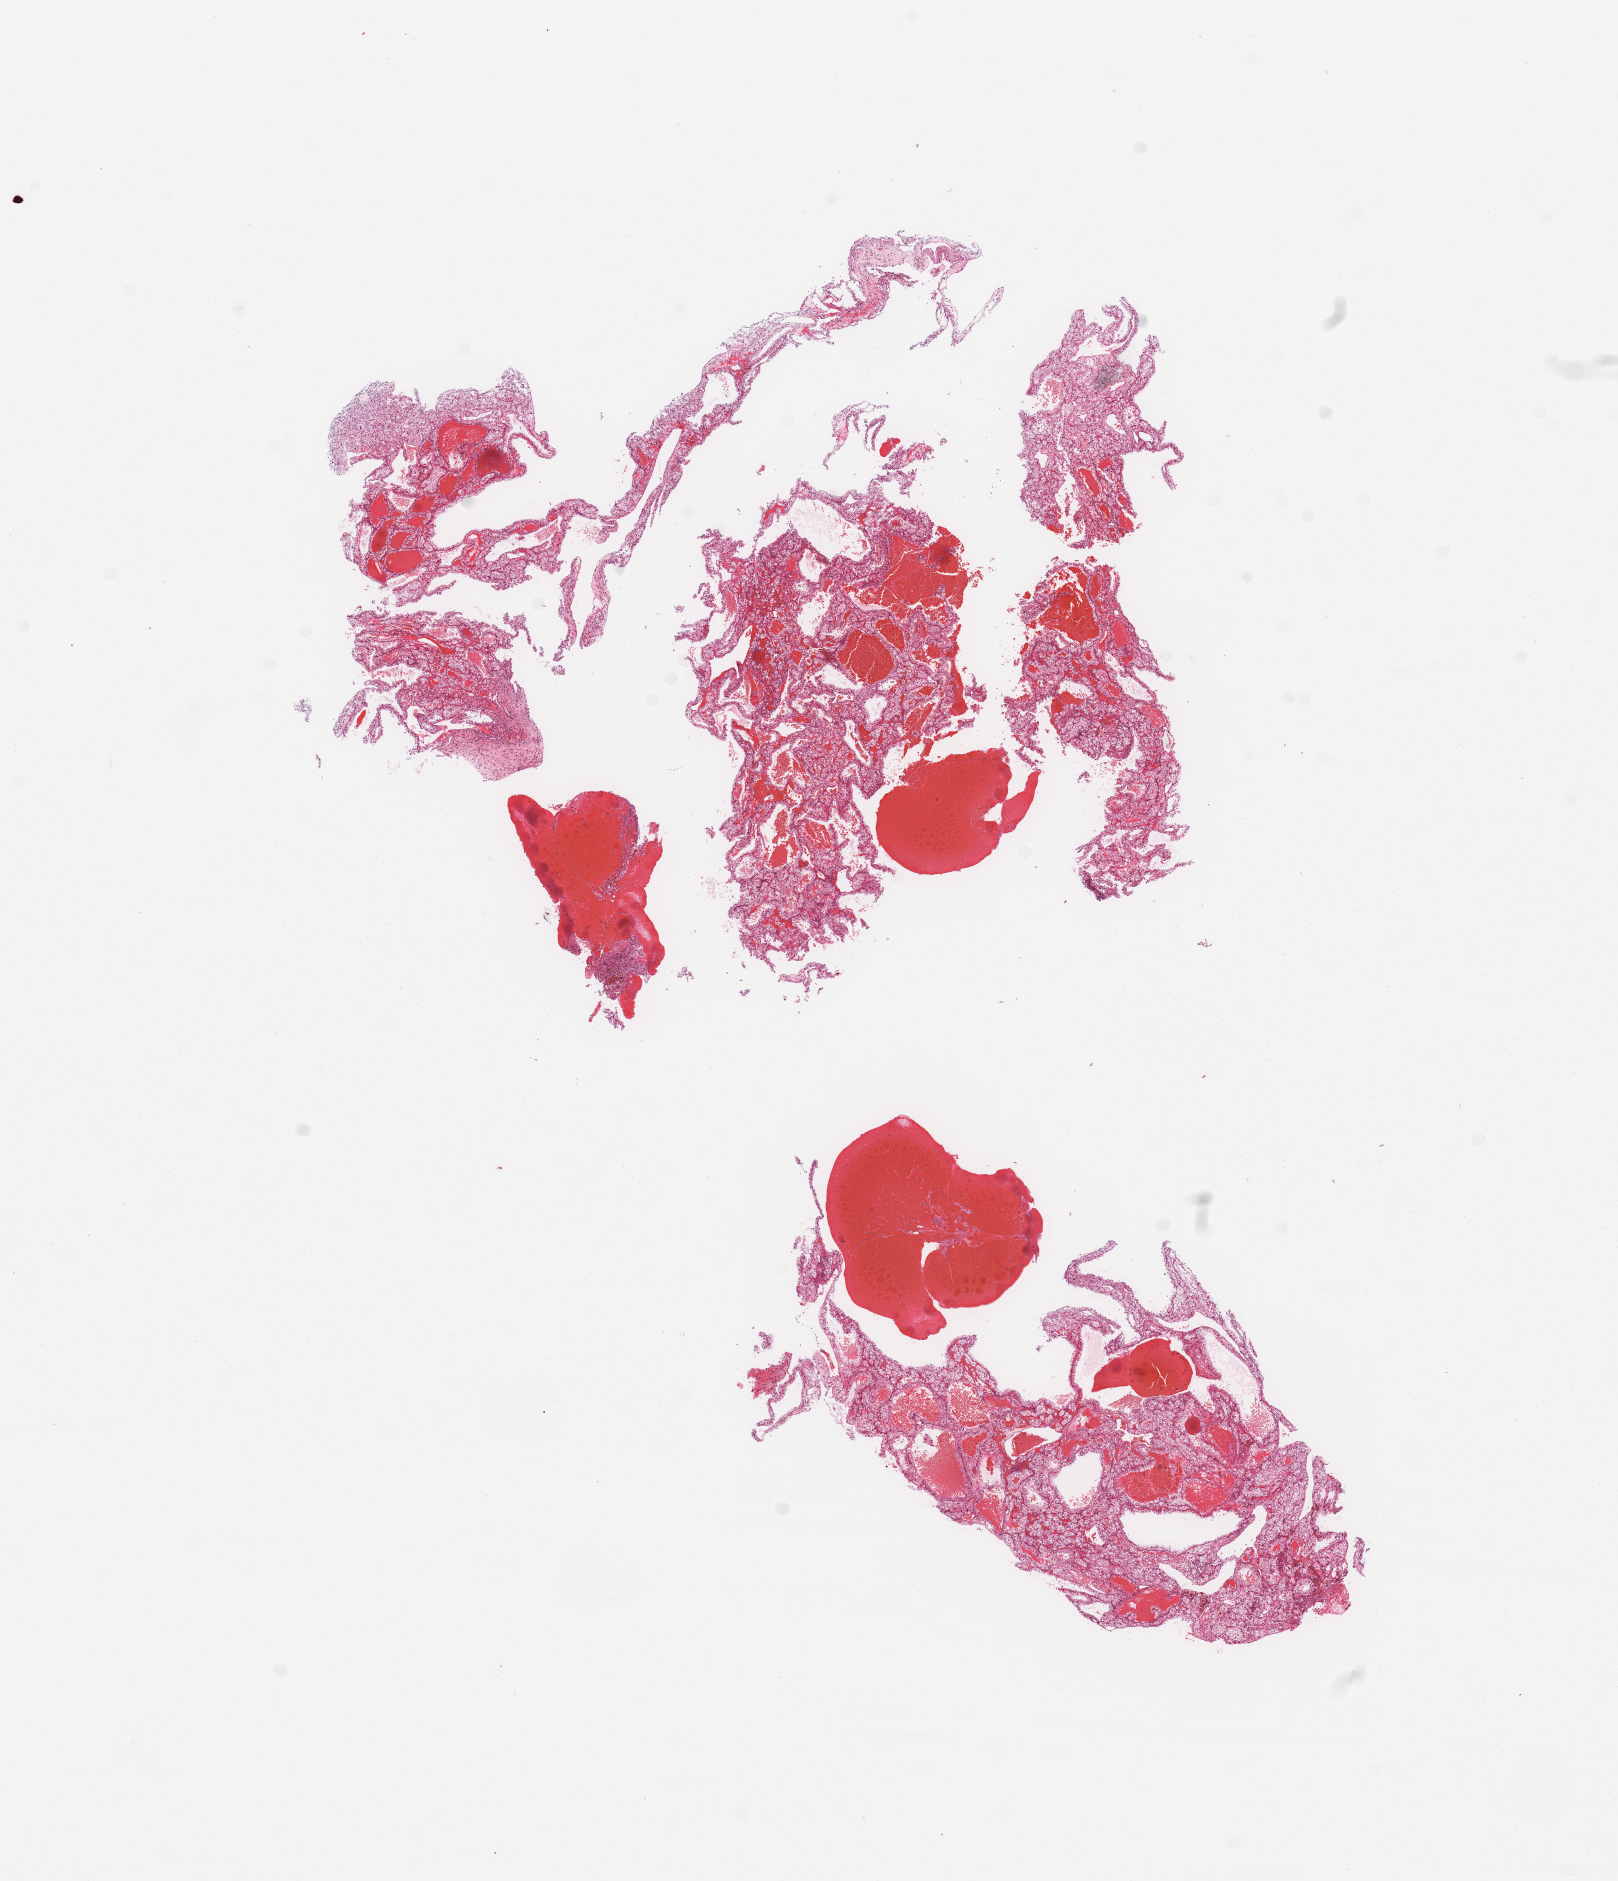
Whole-slide histology image, Hematoxylin and eosin (H&E) stained, shown as a low-resolution overview of the whole scanned area (about 12.8 x 14.9 mm). Tumour tissue sample, sampled site: kidney. 57-year-old male patient. Histologic grade: G3 (poorly differentiated). Composition of this section per pathologist review: tumour nuclei 85%, necrosis 5%.
• primary tumour site (as recorded): upper pole
• AJCC pathologic stage: I
• diagnosis: Renal cell carcinoma, NOS